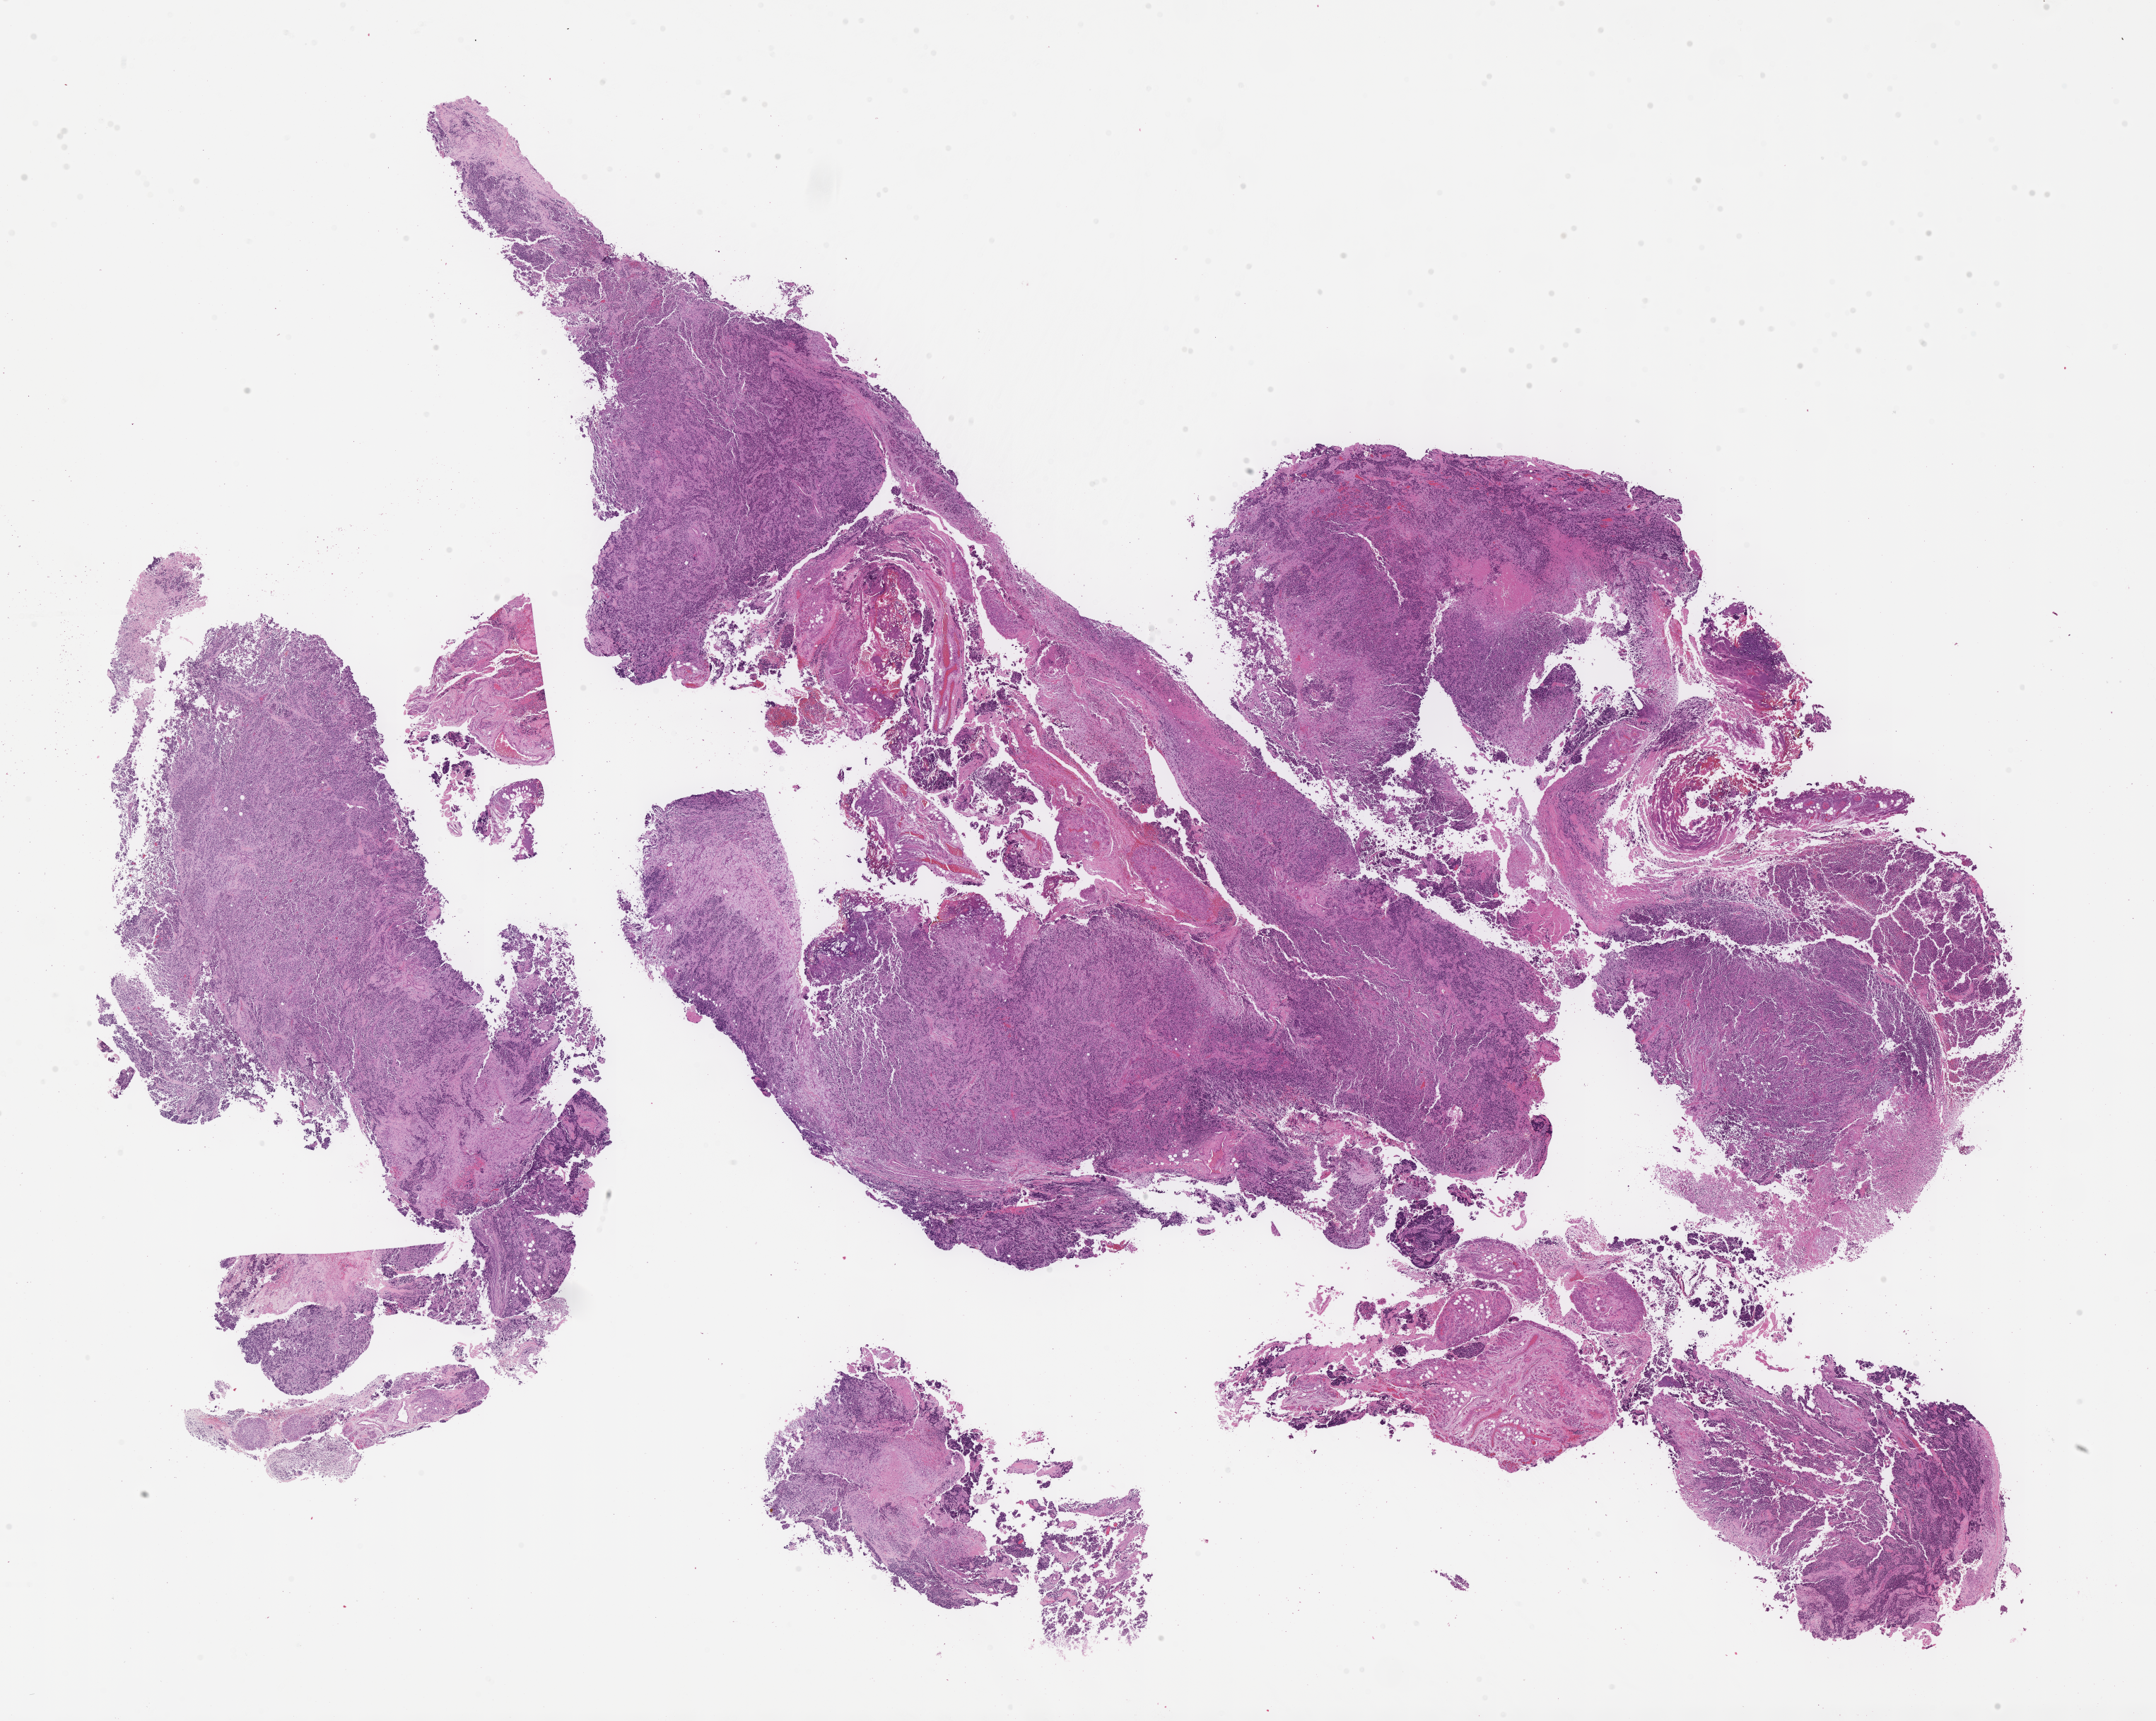
Whole-slide image, hematoxylin and eosin (H&E) stain of tumor tissue, shown as a low-resolution overview of the whole scanned area (about 24.7 x 19.7 mm); FFPE section; sample anatomic site: arm, left axillary. Female patient, age at diagnosis 14.3 years.
Metastatic status at presentation (as recorded): non-metastatic. Diagnosis: rhabdomyosarcoma; histological classification: alveolar rhabdomyosarcoma. Stage (as recorded): 3.